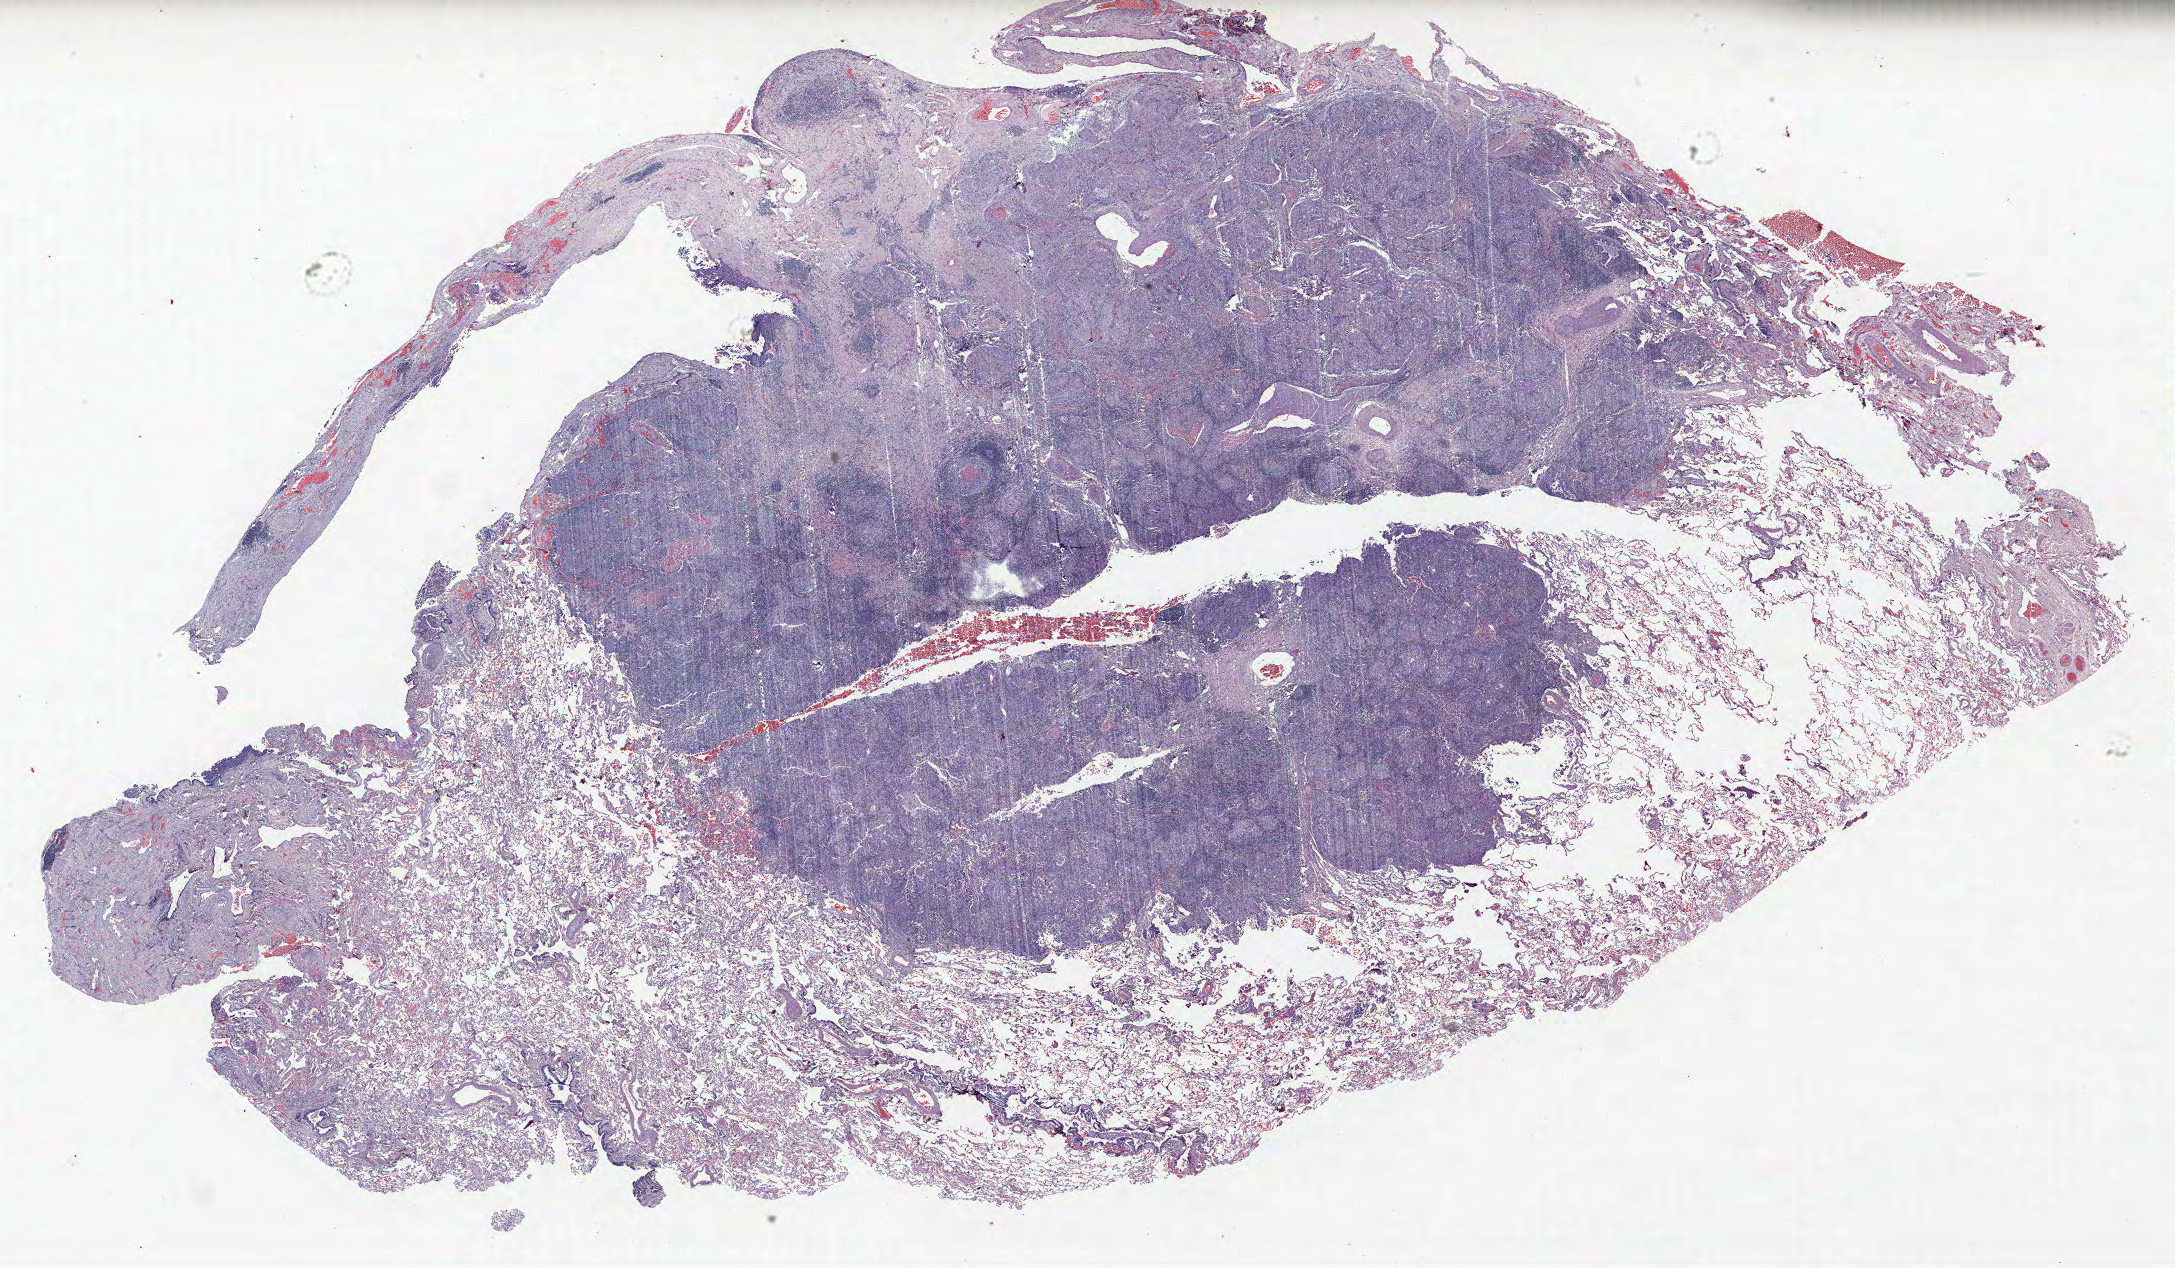
H&E whole-slide image, low-resolution overview of the scanned area, about 34.8 x 20.3 mm (acquisition: 40x scan). FFPE section. Lung. Male, age 61 at enrolment. Former smoker at enrolment. Grade: poorly differentiated (G3).
• tumour size (pathology): 20 mm
• ICD-O-3 topography: upper lobe of lung (C34.1)
• primary tumour location (clinical record): right upper lobe
• participant's lung-cancer diagnosis: Squamous cell carcinoma, NOS
• stage (AJCC 6th edition): IA